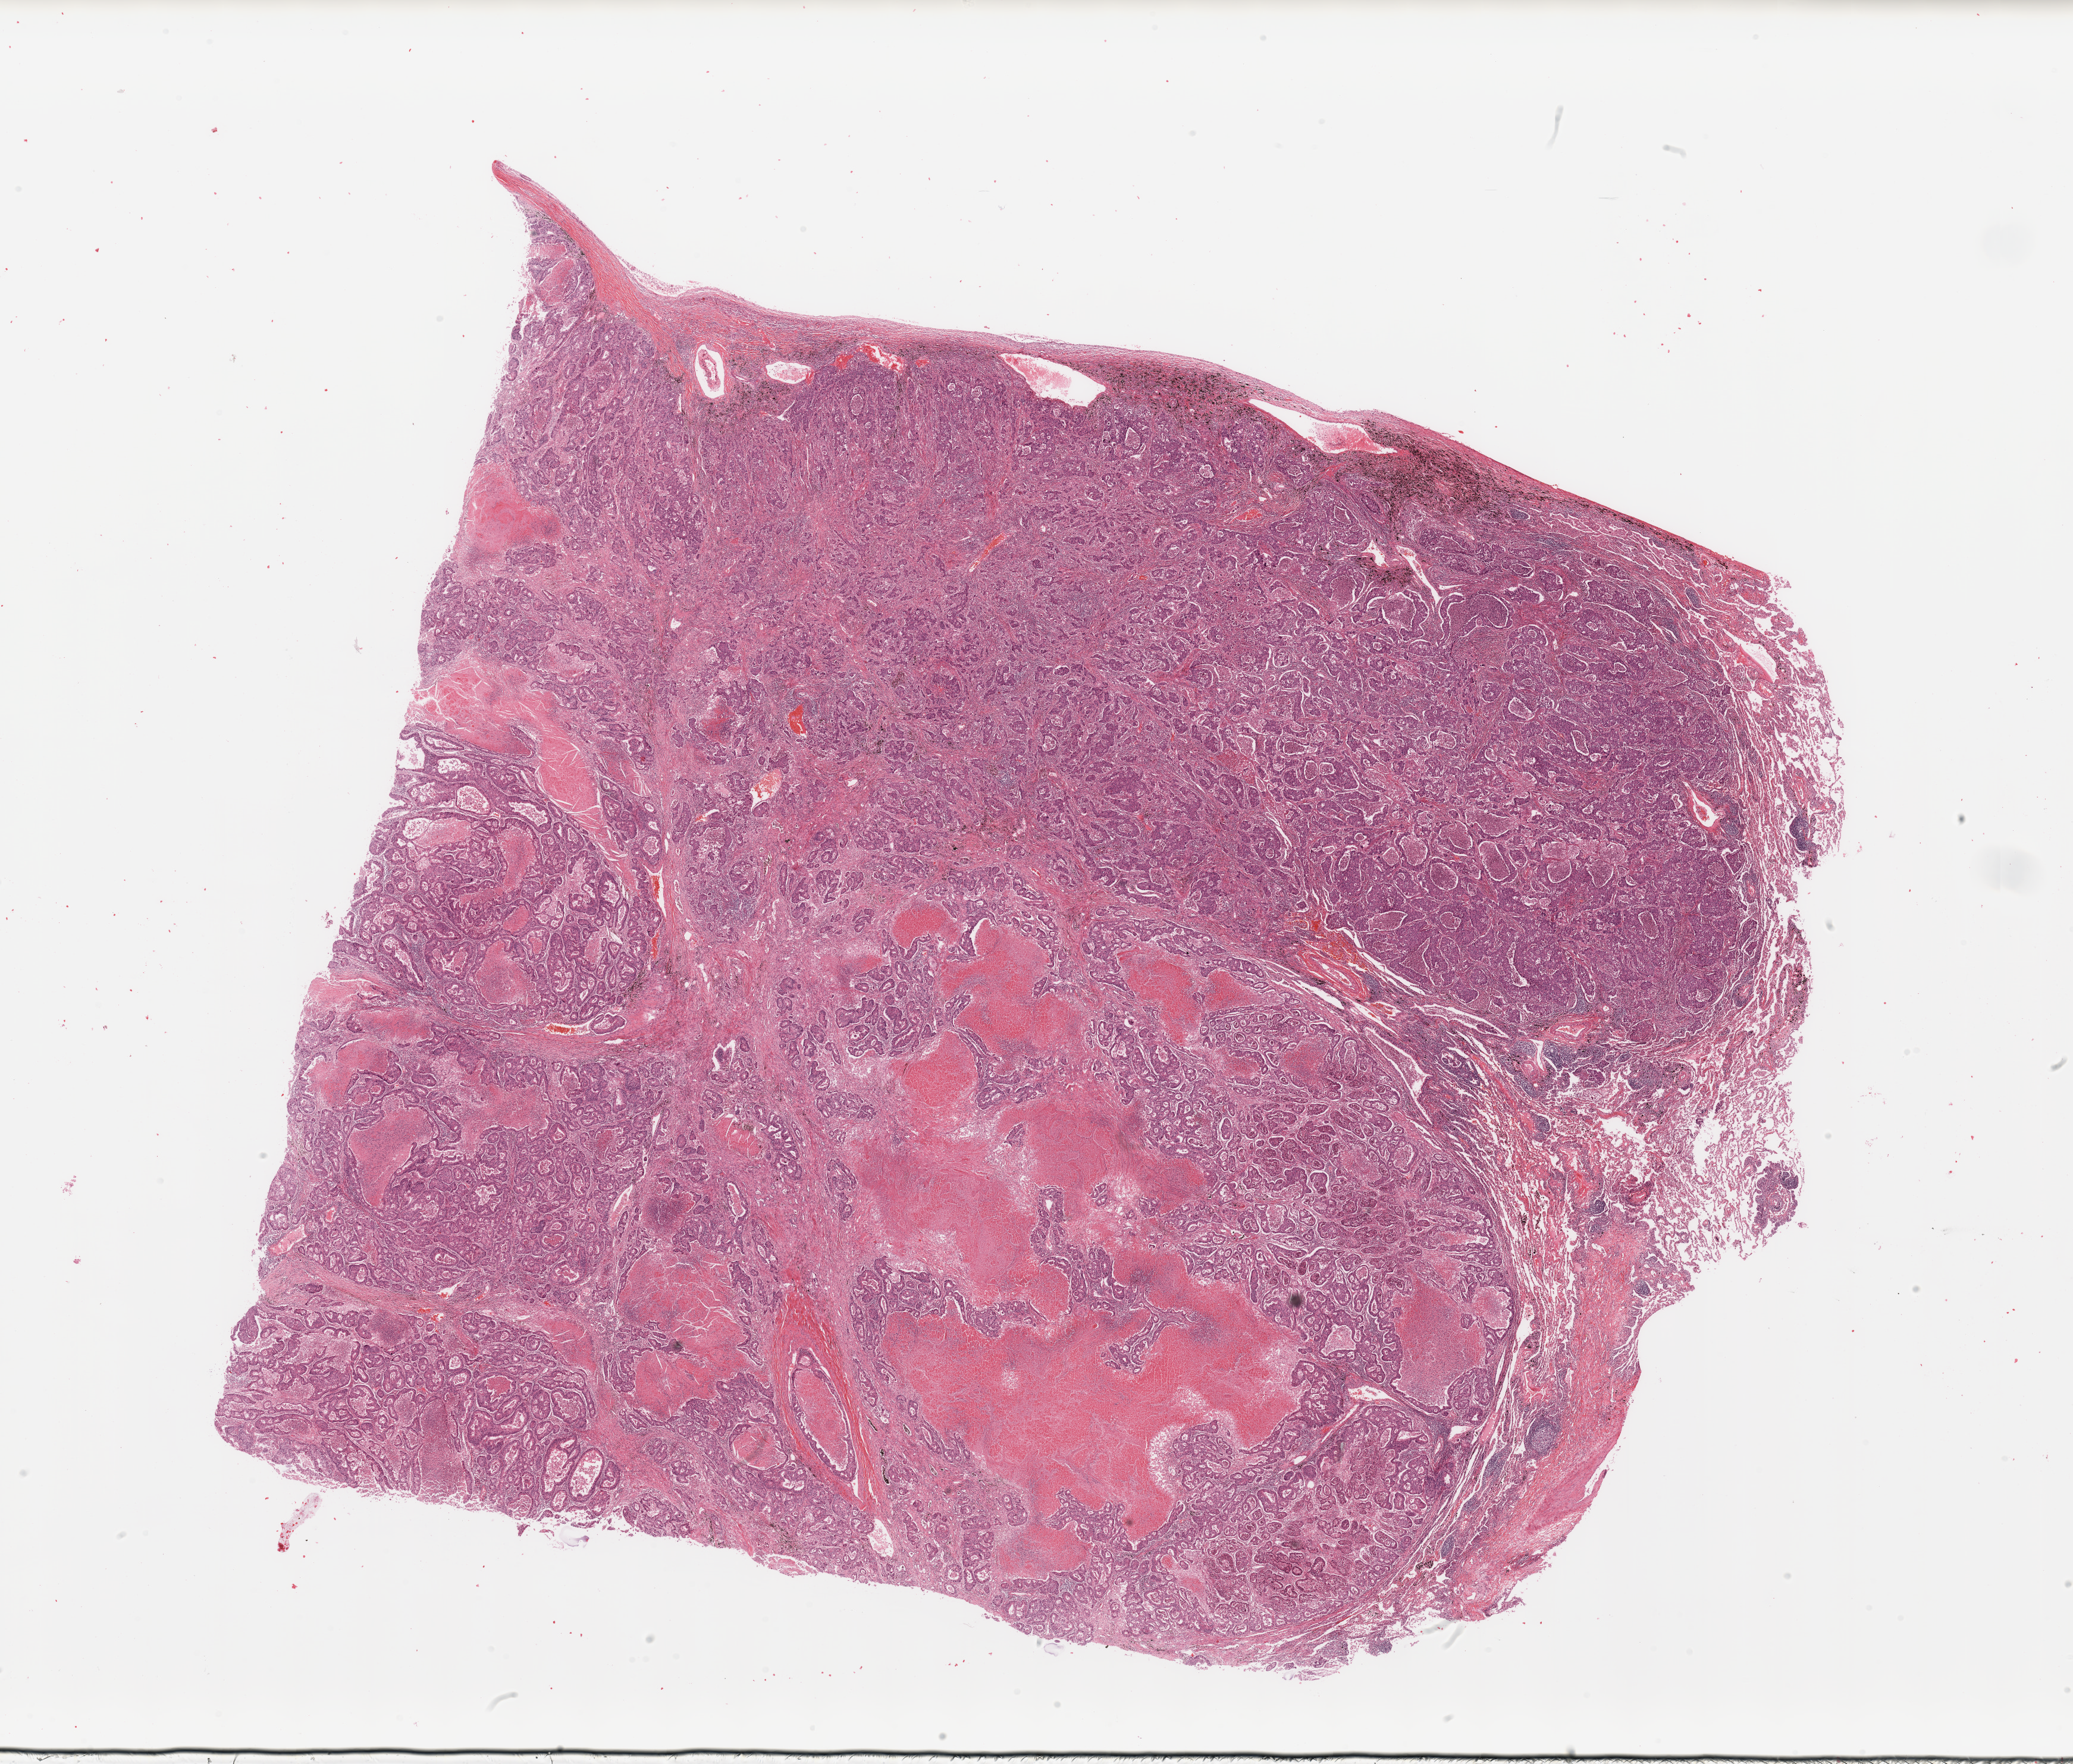
Whole-slide histology image, H&E, shown as a low-resolution overview of the whole scanned area (about 27.6 x 23.5 mm); tumour tissue sample, lung. Male, 76 y/o. Histologic grade: G3 (poorly differentiated).
AJCC pathologic stage: IB. Diagnosis: Adenocarcinoma, NOS.